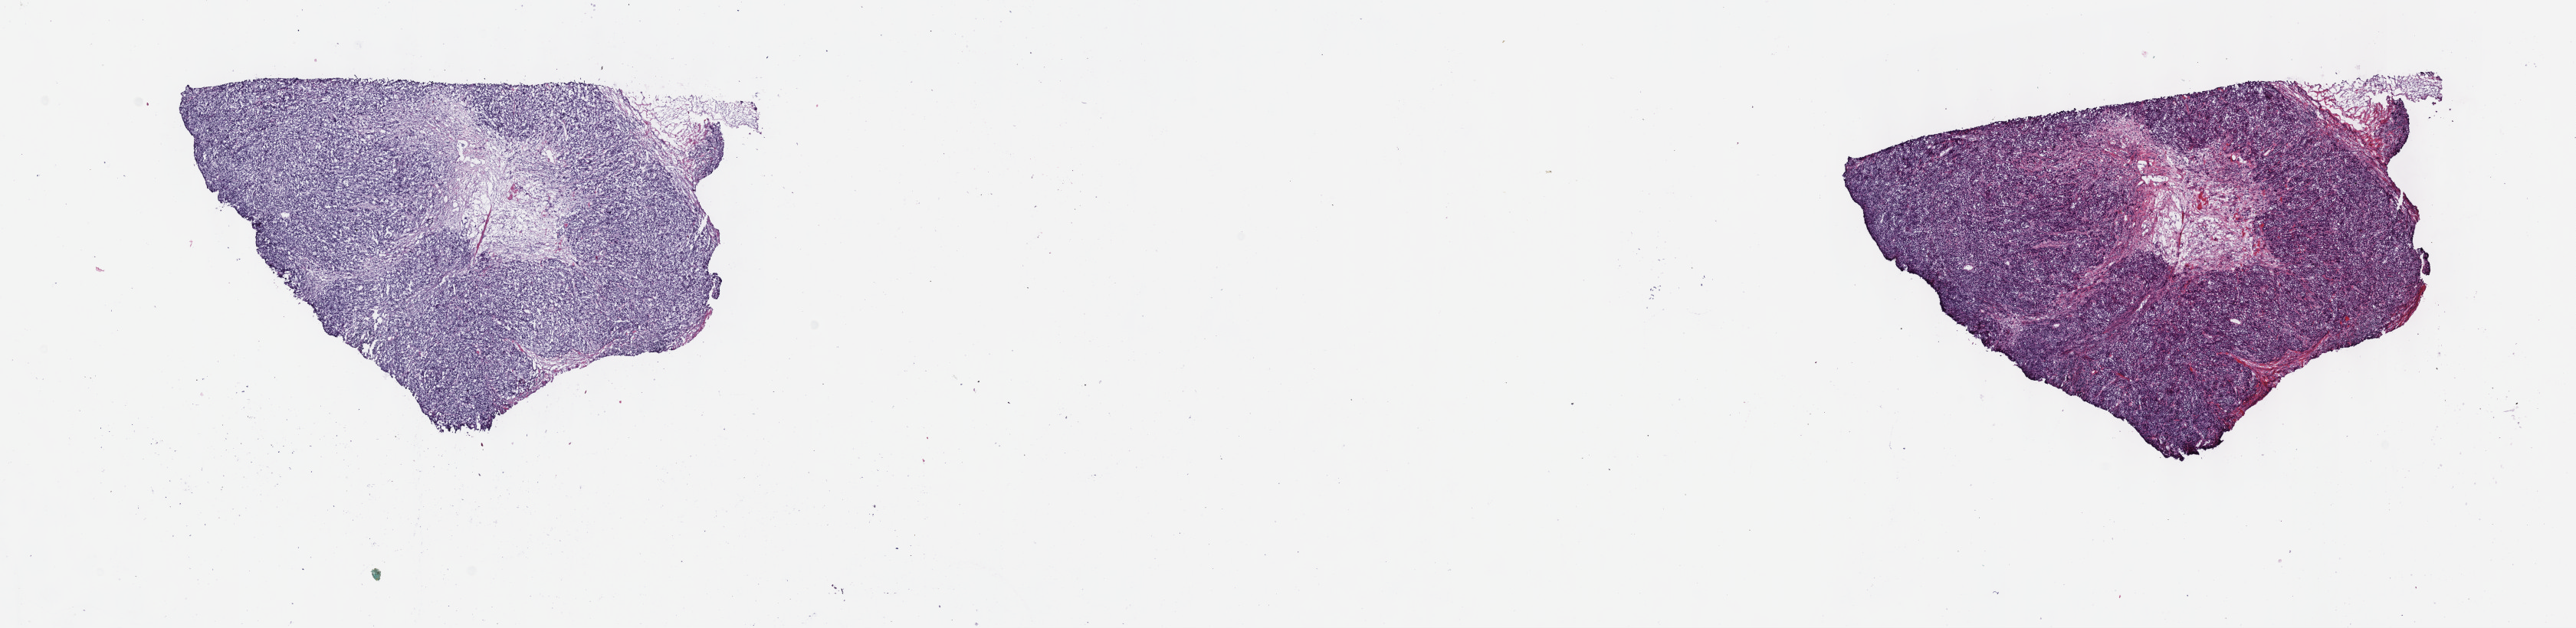
Whole-slide histology image, H&E — whole scanned area (about 27.2 x 6.6 mm, from a 40x scan) shown as a low-resolution overview; frozen section; metastatic tumour sample, sampled site: lymph nodes of inguinal region or leg. Male, age 70 years at initial diagnosis. Composition of this section per pathologist review: tumour cells 85%, tumour nuclei 80%.
This section: metastatic tumour tissue. Patient diagnosis: Nodular melanoma.